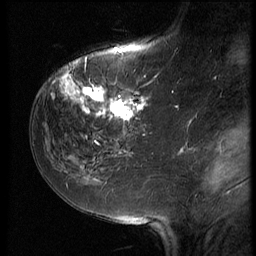
Breast MRI (dynamic contrast-enhanced), one sagittal slice; slice 21 of 64 in the series (ordered by position); 3 images stored at this slice position (order not interpretable as contrast timing); 1.5 T; TE 4.2 ms, TR 9 ms; 2.5 mm slice thickness; 256 × 256 image matrix, field of view 180 × 180 mm. Female patient, age 59 years. From the clinical record (not read from this slice): setting: breast cancer imaged before/during neoadjuvant chemotherapy; receptor status: HER2-positive.
Outlined on this slice (semi-automatic segmentation, software-assisted and operator-edited):
- analysis volume of interest (the breast-tissue region the enhancement analysis was run in; not a lesion): bounding box [x1, y1, x2, y2] px = [54, 65, 155, 132]
- tumour enhancement mask (voxels above the 140 % enhancement threshold inside the analysis volume of interest): [54, 65, 149, 122]